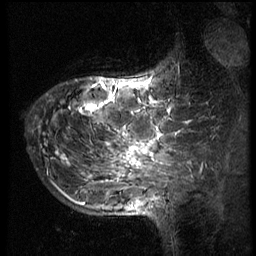
Breast MRI (dynamic contrast-enhanced), one sagittal slice; 3 images stored at this slice position (order not interpretable as contrast timing); 1.5 T; TE 4.2 ms, TR 8.9 ms; 256 × 256 image matrix. Female patient, age 39 years. Case-level facts recorded for this patient, not image findings: setting: breast cancer imaged before/during neoadjuvant chemotherapy; receptor status: HER2-positive.
Outlined on this slice (semi-automatic segmentation, software-assisted and operator-edited):
- analysis volume of interest (the breast-tissue region the enhancement analysis was run in; not a lesion): bounding box (x1, y1, x2, y2) in pixels: (29, 54, 166, 196)
- tumour enhancement mask (voxels above the 140 % enhancement threshold inside the analysis volume of interest): (56, 75, 159, 181)